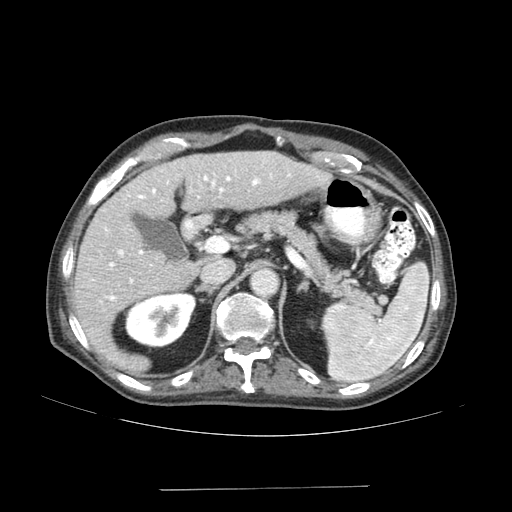
Contrast-enhanced abdominal CT (liver protocol), one axial slice; reconstruction kernel SOFT; 120 kVp; soft-tissue window (W 400 / L 40 HU); 512 × 512 image matrix, field of view 400 × 400 mm. Case-level facts recorded for this patient, not image findings: diagnosis: hepatocellular carcinoma (patient treated with transarterial chemoembolisation; whether this scan precedes or follows treatment is not stated here); TNM stage (as recorded): Stage-IVA; Child-Pugh class: A; tumour differentiation: poorly differentiated; tumour nodularity: uninodular.
Outlined on this slice (semi-automatically segmented with operator editing):
- liver parenchyma outside the tumour (the mass and vessels are separate outlines, so this box may not span the whole liver): bounding box <72,150,330,370> (left, top, right, bottom; pixels)
- liver vessels: <105,174,290,301>